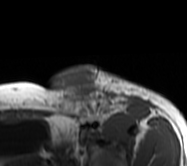
MRI of an extremity soft-tissue mass, one axial slice; position 45 of 62 along the scan axis; MR volume resampled by the dataset authors to the PET/CT grid (not the native acquisition matrix); 3.27 mm slice thickness; 187 × 166 image matrix, field of view 183 × 162 mm. Female patient. From the clinical record (not read from this slice): histological type: leiomyosarcoma; grade: high; site of the primary tumour: groin.
Outlined on this slice (expert contour drawn on MRI and transferred to this co-registered scan by the dataset authors):
- gross tumour volume including surrounding oedema: bounding box <50,65,154,121> (left, top, right, bottom; pixels)
- gross tumour volume (mass): <50,65,110,120>